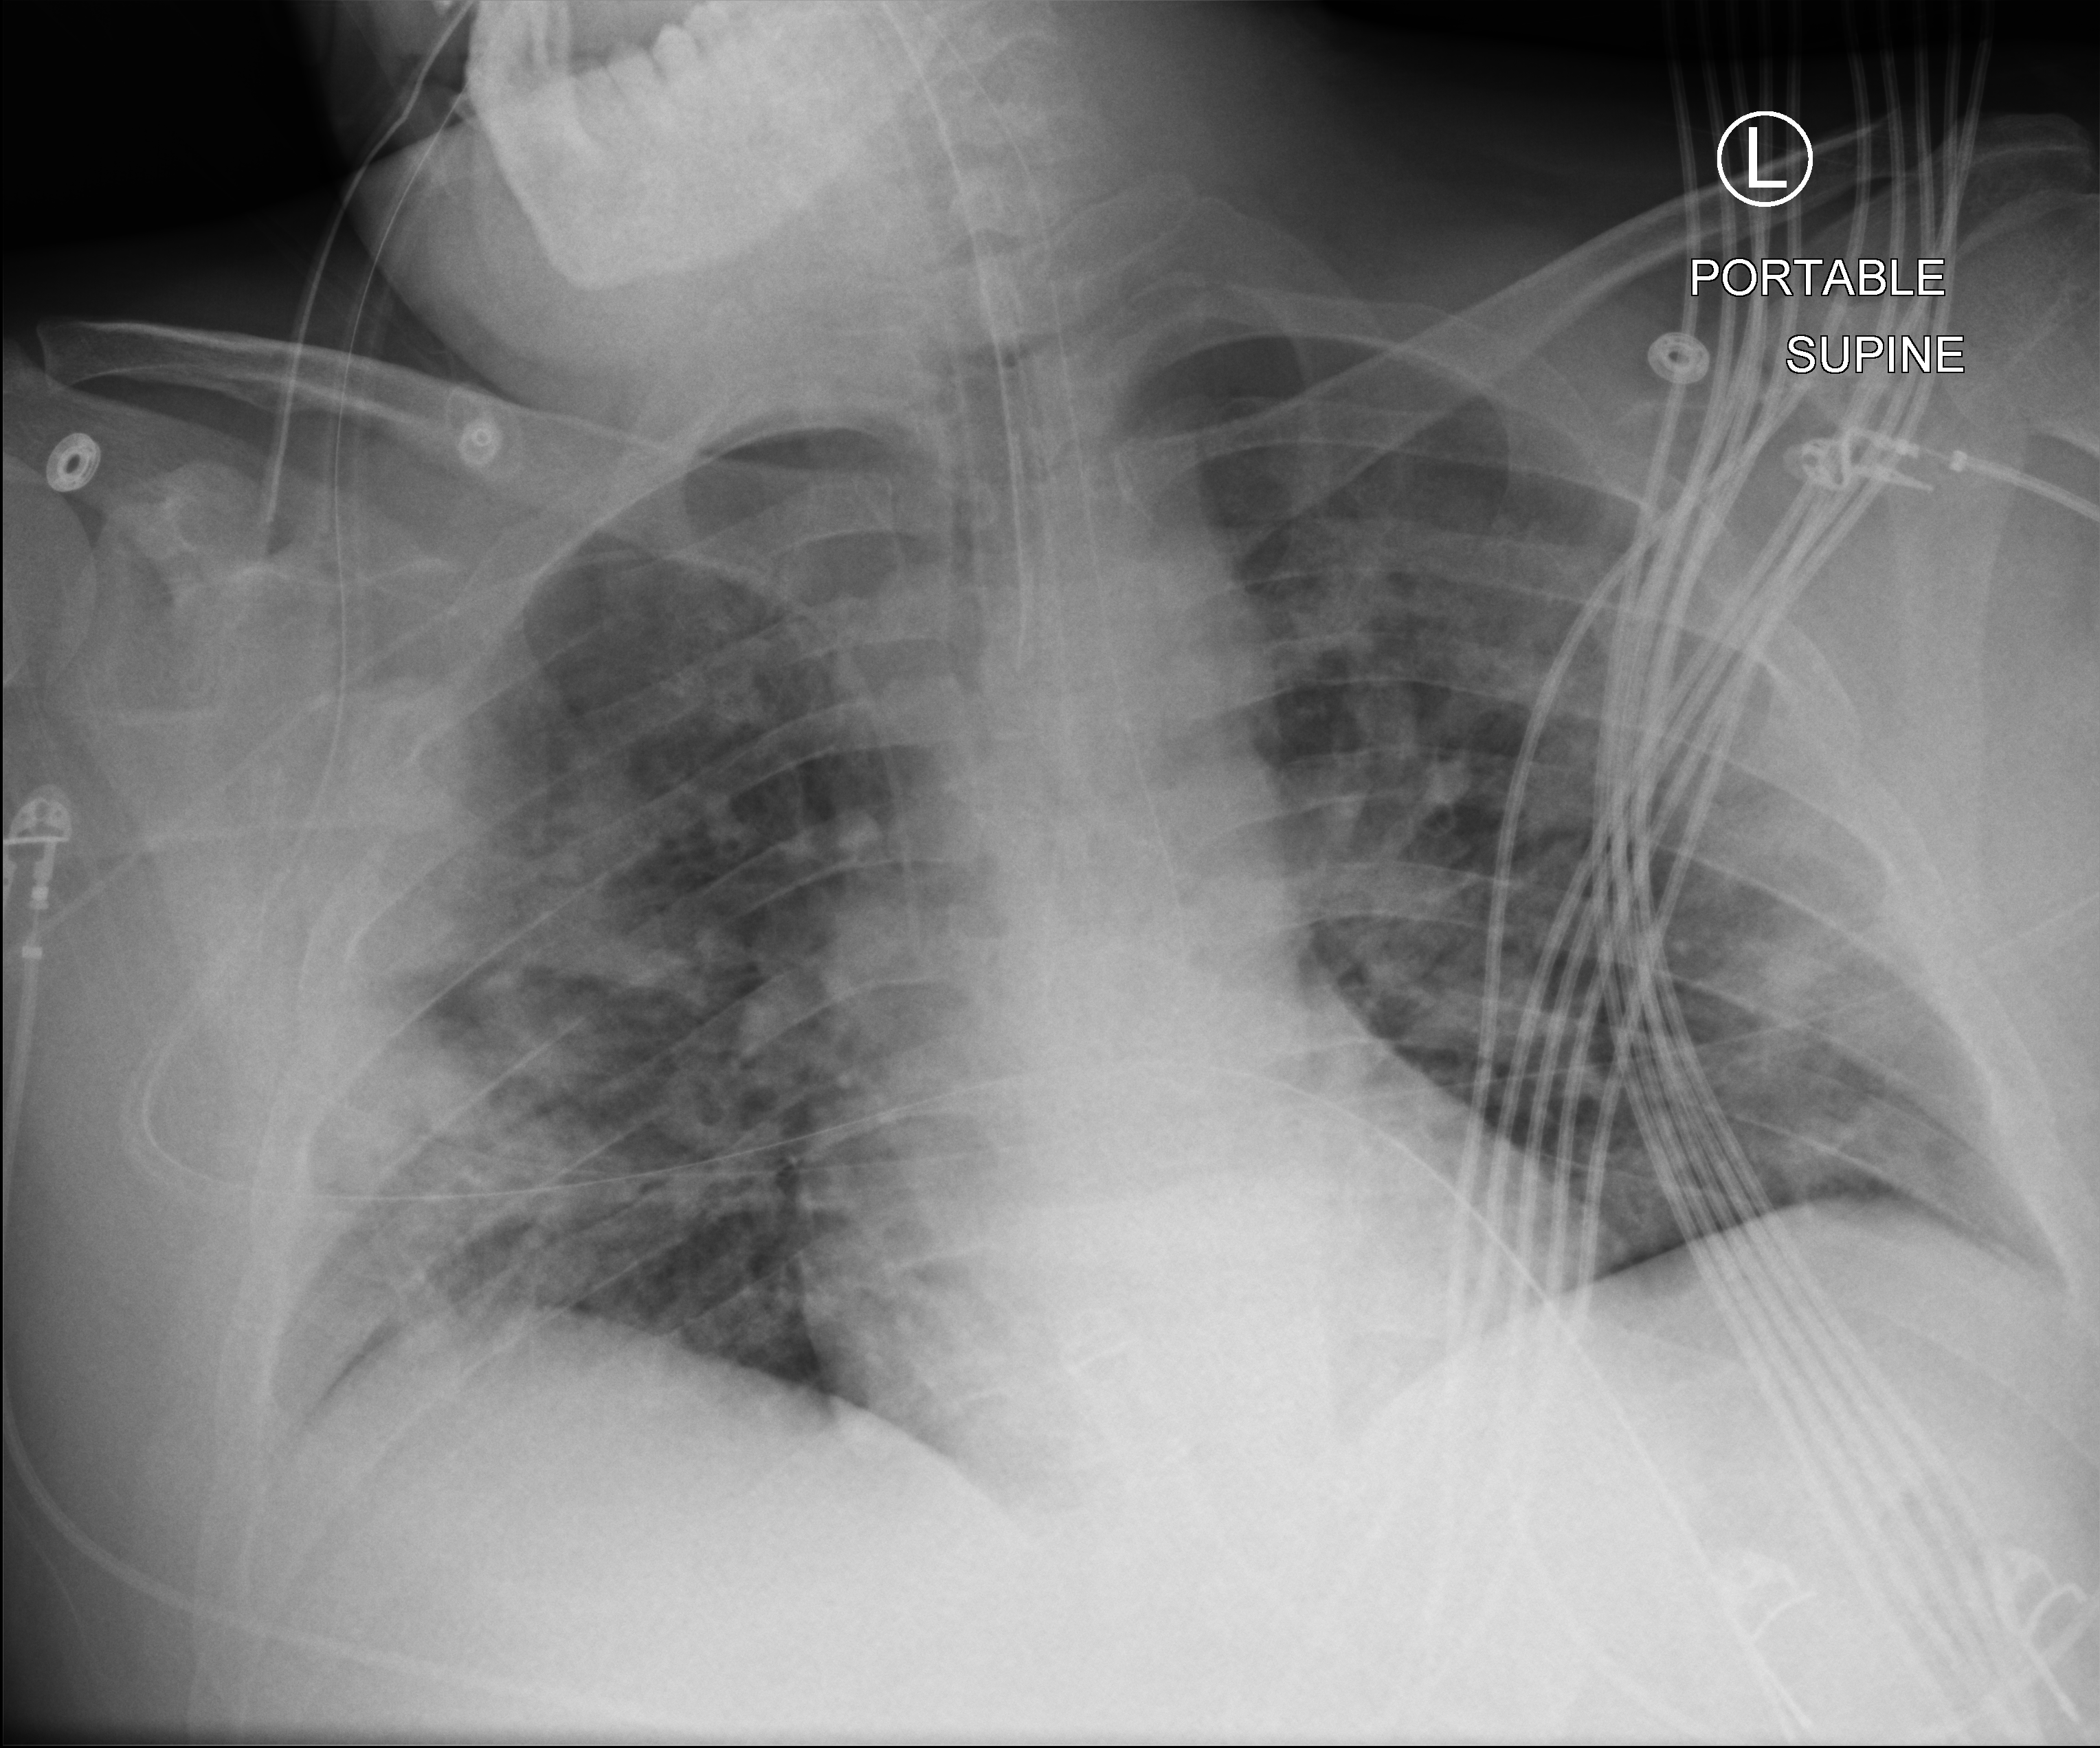
Portable chest radiograph; anteroposterior (AP) projection. Female patient hospitalised with COVID-19, age 18–59 years.
From the hospital-stay record, not from the radiograph (when in the stay this image was taken is not recorded):
- mechanically ventilated during this hospital stay: yes
- admitted to intensive care during this hospital stay: yes
- length of hospital stay: 16 days